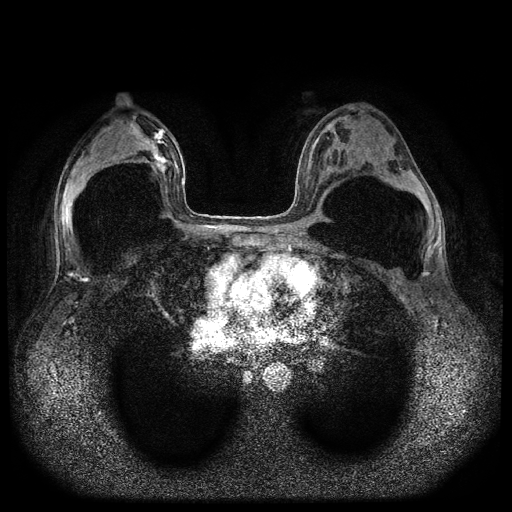
Breast MRI (dynamic contrast-enhanced, multi-phase), one axial slice; slice 50 of 116 in the series (ordered by position); dynamic contrast-enhanced series, time point 2 of 5 at this slice position (early post-contrast); 1.5 T; TE 2.6 ms, TR 5.4 ms; 2 mm slice thickness; 512 × 512 image matrix. Female patient, age 42 years.
Structures marked on this image (semi-automatically segmented with operator editing):
- breast lesion (labelled 'tumour' in the annotation; benign lesions carry a separate 'benign' label): bounding box (x1, y1, x2, y2) in pixels: (150, 129, 169, 166)